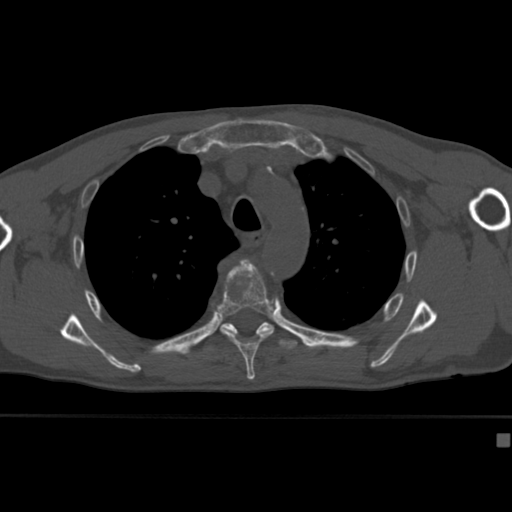
CT including the spine, one axial slice; position 306 of 430 along the scan axis; reconstruction kernel Br40s; 120 kVp; bone window (W 1800 / L 400 HU); 1.5 mm slice thickness; 512 × 512 image matrix, field of view 337 × 337 mm. Male patient, age 64 years. Case-level facts recorded for this patient, not image findings: primary cancer: uterus.
Structures marked on this image (semi-automatic segmentation, software-assisted and operator-edited):
- T4 vertebra: bounding box <233,258,251,269> (left, top, right, bottom; pixels)
- T5 vertebra: <217,262,273,382>
- T6 vertebra: <203,322,298,352>